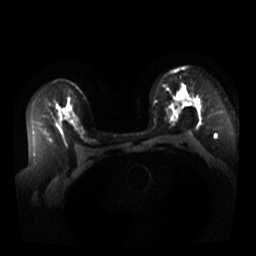
Breast MRI, one axial slice; slice 23 of 44 in the series (ordered by position); diffusion-weighted series; image 2 of 4 stored at this slice position (different b-values; order by instance number); 3 T; 5 mm slice thickness; 256 × 256 image matrix, field of view 340 × 340 mm. Female patient.
Annotated regions visible in this slice (outlined manually by an expert reader):
- tumour on diffusion-weighted imaging: bounding box [x1, y1, x2, y2] px = [180, 98, 187, 102]